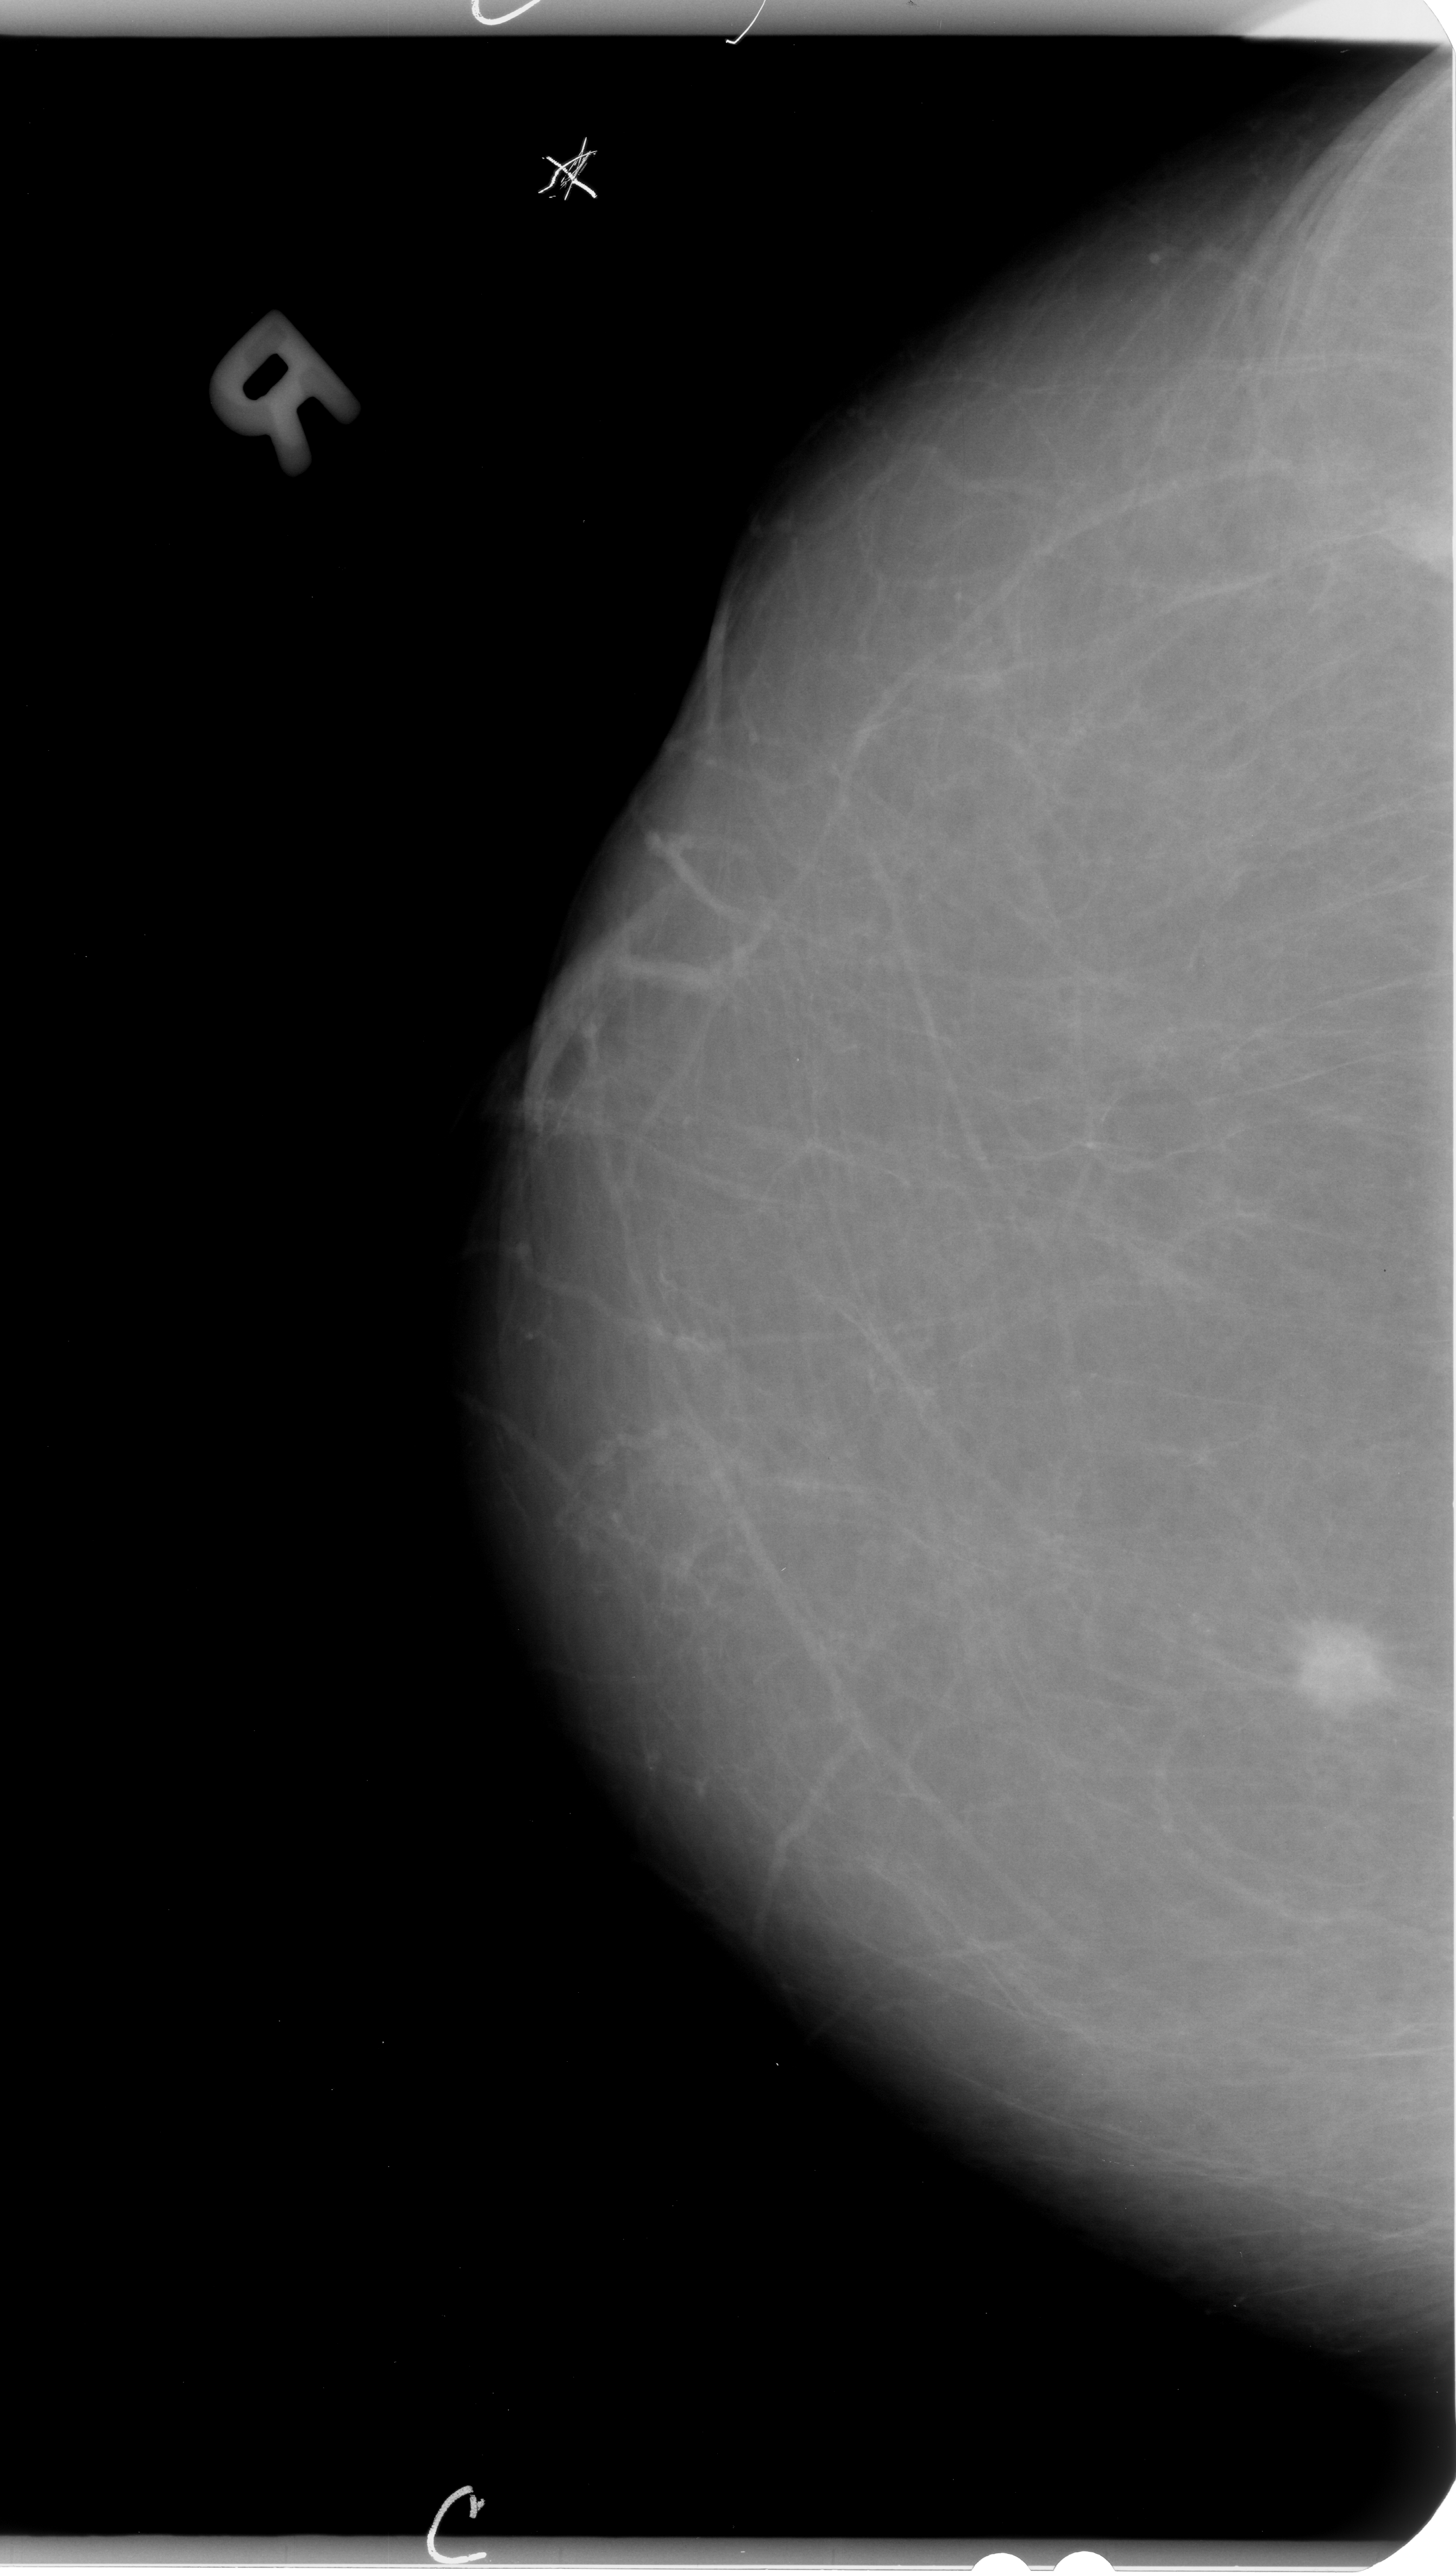
Mammogram (digitized film); right breast; CC view; breast composition: almost entirely fatty (BI-RADS density category 1 of 4).
Finding: mass, shape irregular, margins spiculated; BI-RADS assessment category 4; subtlety rating 5 on a 1 (subtle) to 5 (obvious) scale; pathology result (as recorded, not read from the image): malignant.